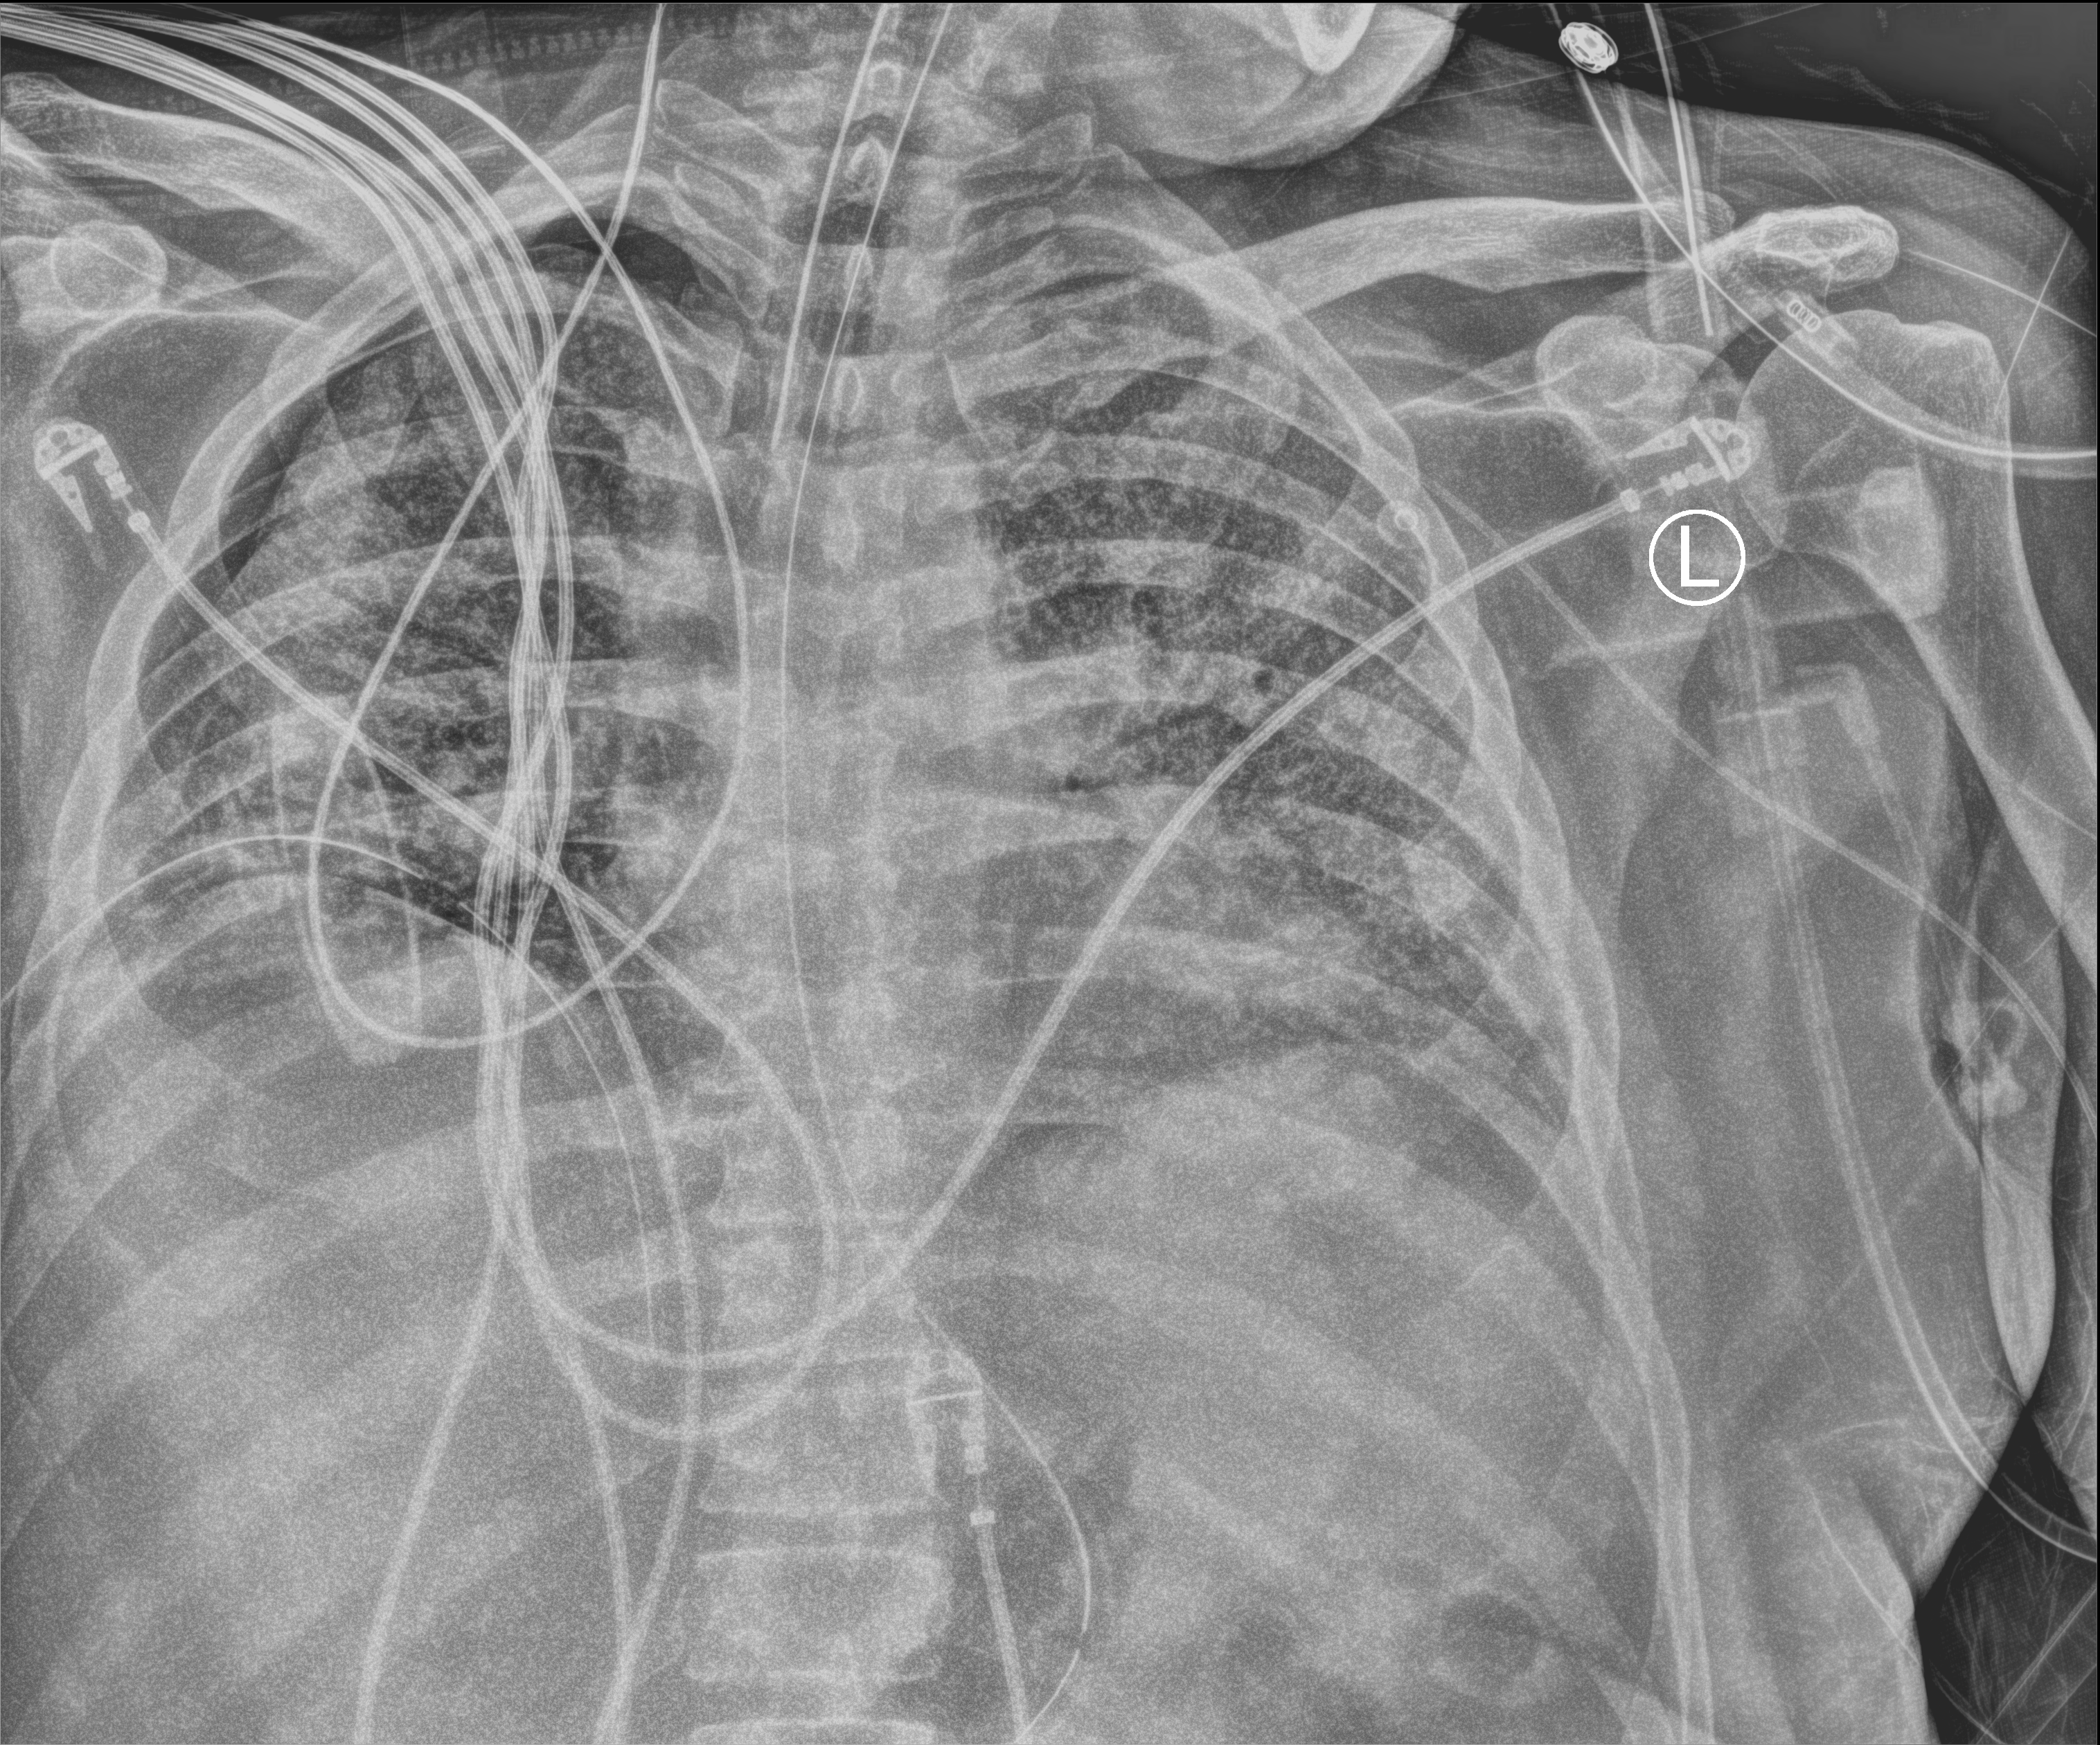
Bedside chest radiograph (computed radiography), anteroposterior (AP) projection. Patient hospitalised with COVID-19; male, aged 18–59 years.
Admission-level facts for this patient (not findings on this image; timing relative to this image not recorded): mechanically ventilated during this hospital stay: yes; admitted to intensive care during this hospital stay: yes; length of hospital stay: 80 days.